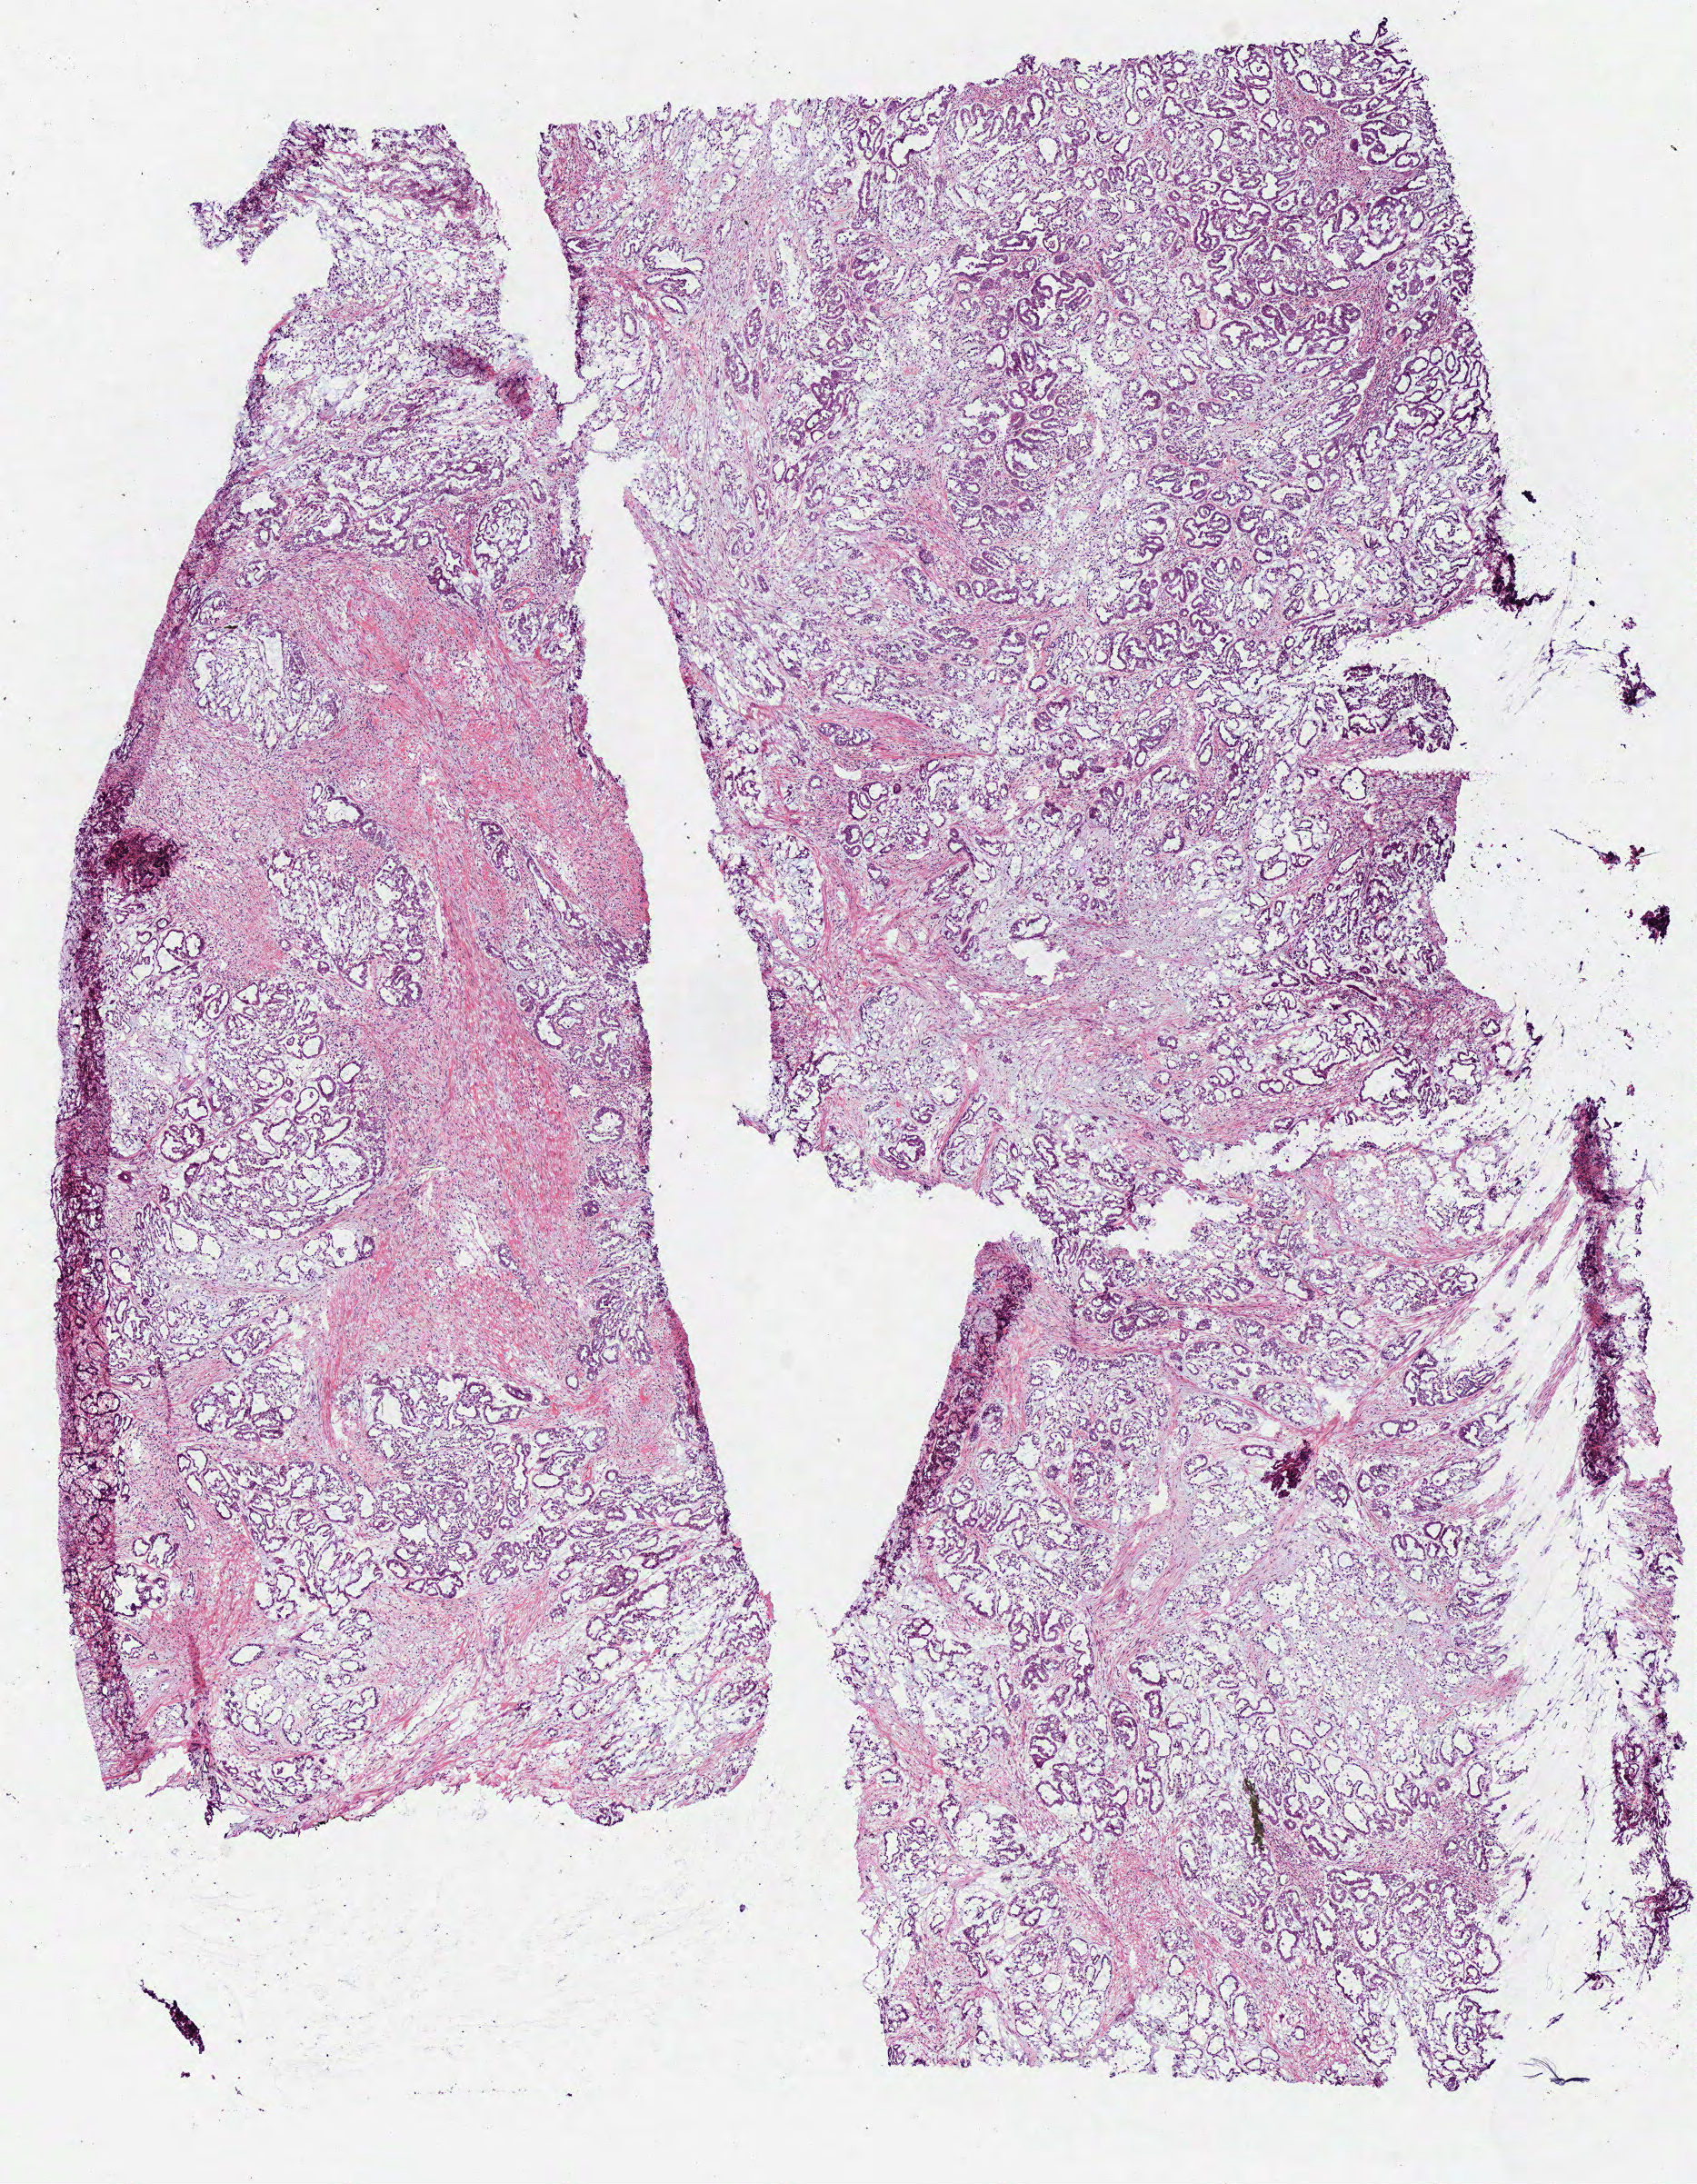
Digitized H&E-stained tissue section (whole slide), a low-resolution overview of the entire scanned area, about 7.3 x 9.4 mm, frozen section from the bottom of the tissue portion, primary tumour sample from the kidney. Female, age 53 years at initial diagnosis. Composition of this section per pathologist review: tumour cells 90%, tumour nuclei 85%, normal cells 0%, stromal cells 10%, necrosis 0%.
Laterality: left. Histologic diagnosis: Papillary adenocarcinoma, NOS. AJCC pathologic stage: IV (6th edition).